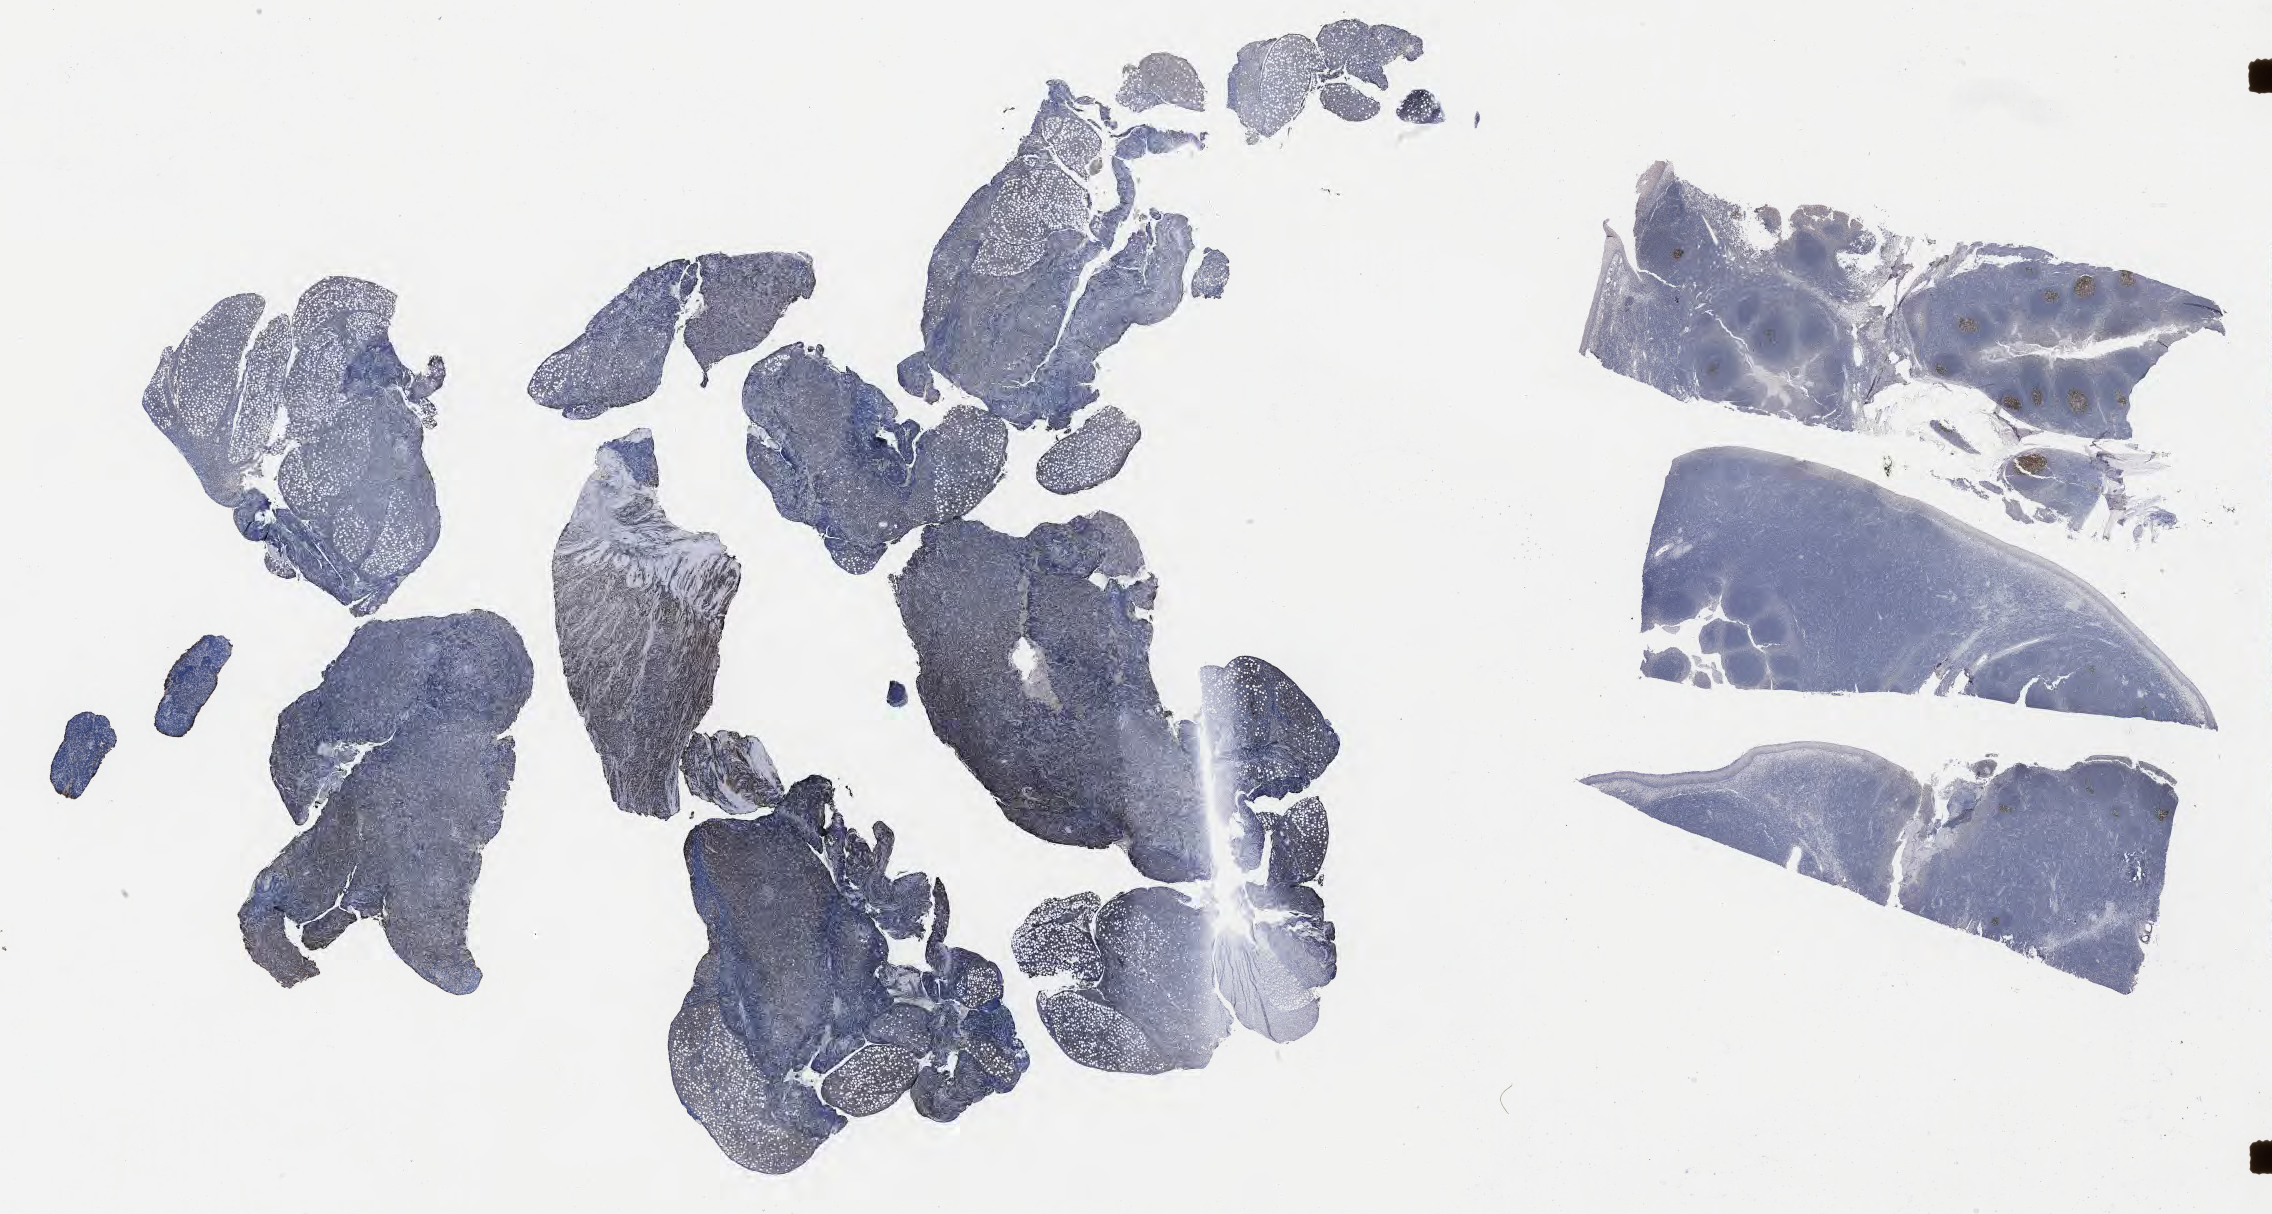
Immunohistochemistry (IHC) whole-slide image stained for BCL6, low-resolution overview of the scanned area, about 36.7 x 19.6 mm, tumor tissue, site: abdomen proper. Male, age 4 years at initial diagnosis.
Diagnosis: Burkitt lymphoma, NOS.